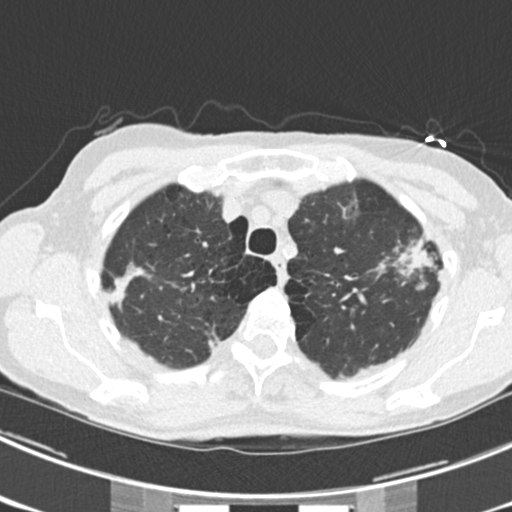
Low-dose screening chest CT, one axial slice; slice 179 of 225 in the series (ordered by position); lung window (W 1500 / L -600 HU); 512 × 512 image matrix, field of view 302 × 302 mm.
Outlined on this slice (expert manual segmentation):
- lesion 1 (tumor, upper lobe of left lung): bounding box [x1, y1, x2, y2] px = [398, 241, 435, 269]